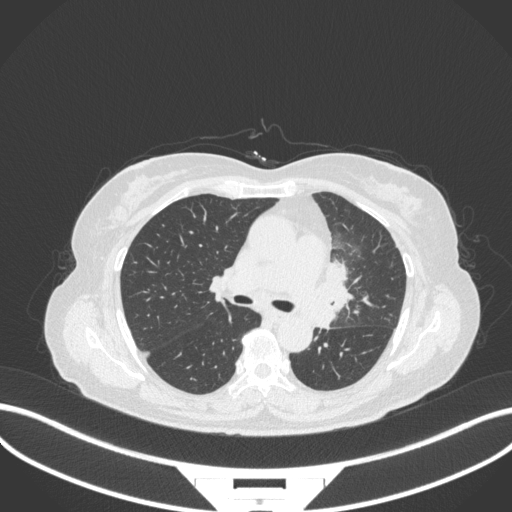
Chest CT, one axial slice. Position 203 of 382 along the scan axis. Lung window (W 1500 / L -600 HU). 1 mm slice thickness. 512 × 512 image matrix. Female patient, age 64 years. Case-level facts recorded for this patient, not image findings: clinical TNM (as recorded): T2a N2 M0.
Structures marked on this image (rectangle marked by the reading radiologist):
- lung tumour (recorded histology: adenocarcinoma): box from (x=314, y=255) to (x=361, y=329) px